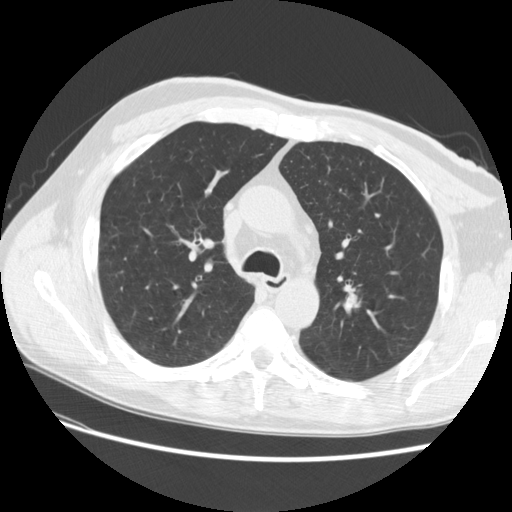
Low-dose screening chest CT, one axial slice; slice 177 of 256 in the series (ordered by position); reconstruction kernel STANDARD; 120 kVp; lung window (W 1500 / L -600 HU); 512 × 512 image matrix, field of view 366 × 366 mm.
Outlined on this slice (manually delineated by an expert):
- lesion 1 (tumor, upper lobe of left lung): bounding box [x1, y1, x2, y2] px = [347, 295, 359, 307]